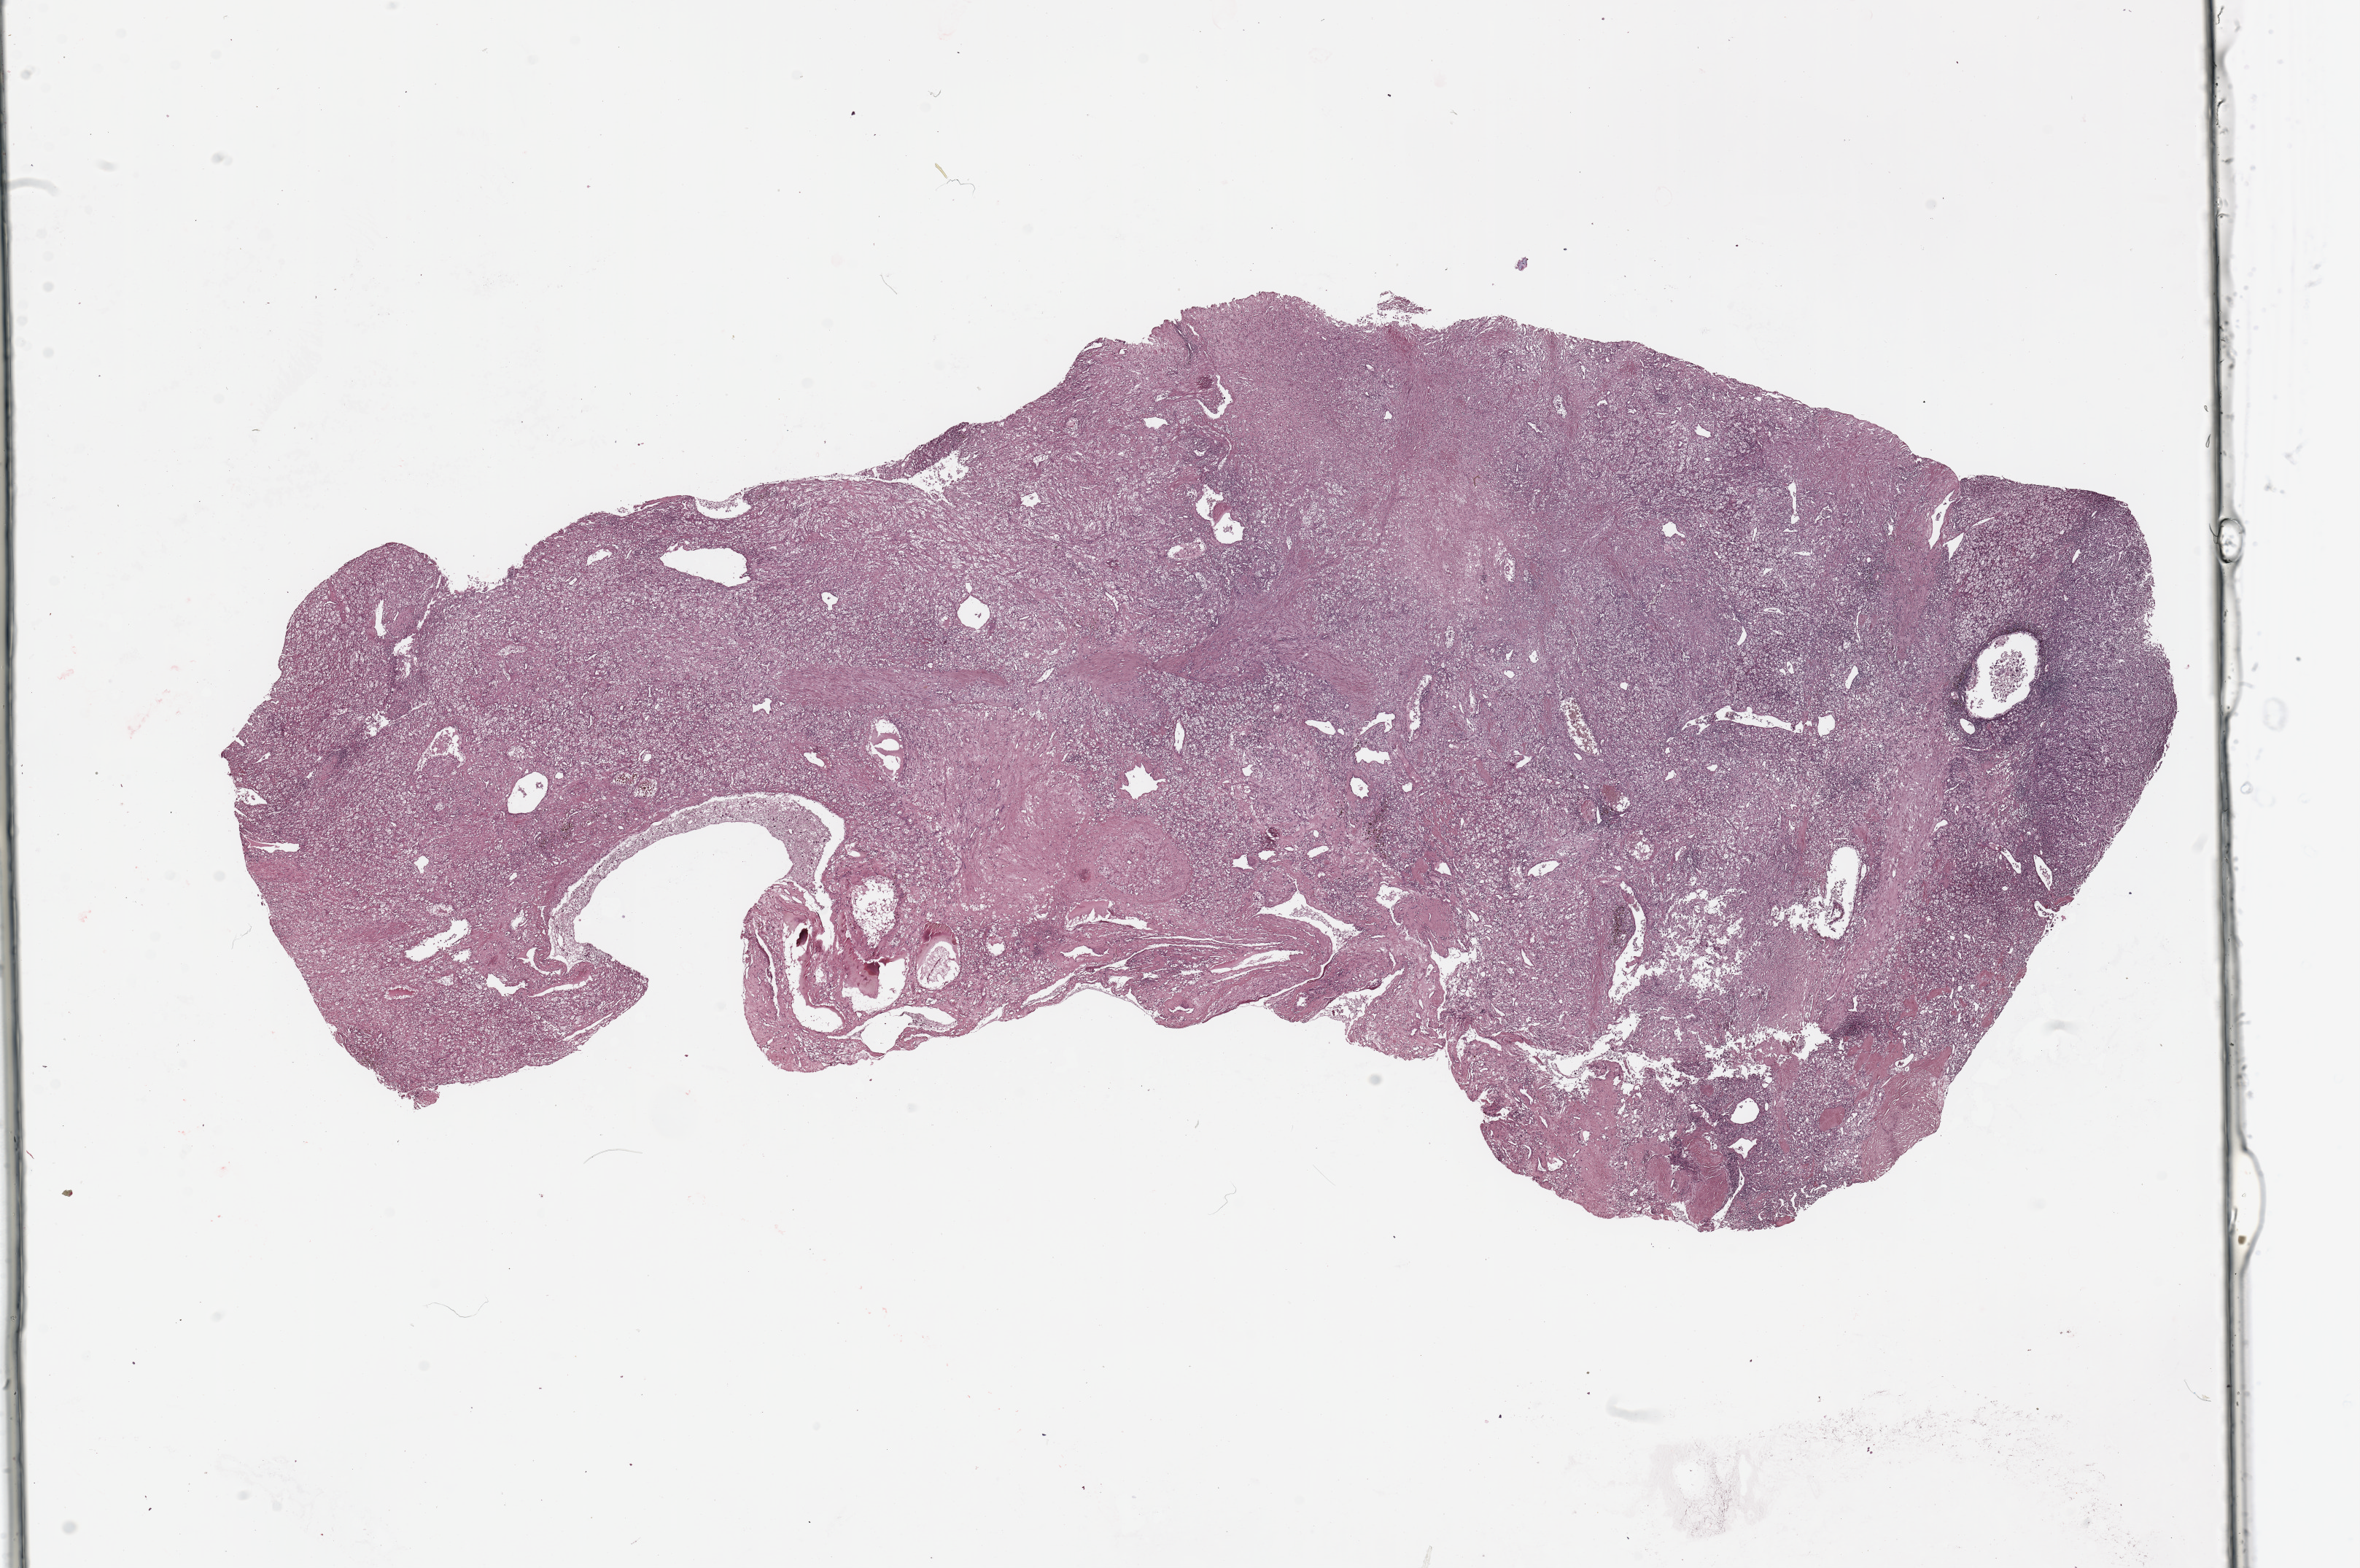
H&E-stained whole-slide image — low-resolution overview of the scanned area, about 25.6 x 17.0 mm, tumour tissue sample, sampled site: kidney. Male, 51 y/o. Histologic grade: G4 (undifferentiated). Pathologist review of this section (percent, as recorded): tumour nuclei 90%, necrosis 10%.
Histologic diagnosis: Renal cell carcinoma, NOS. Primary tumour site (as recorded): middle. AJCC pathologic stage: IV.